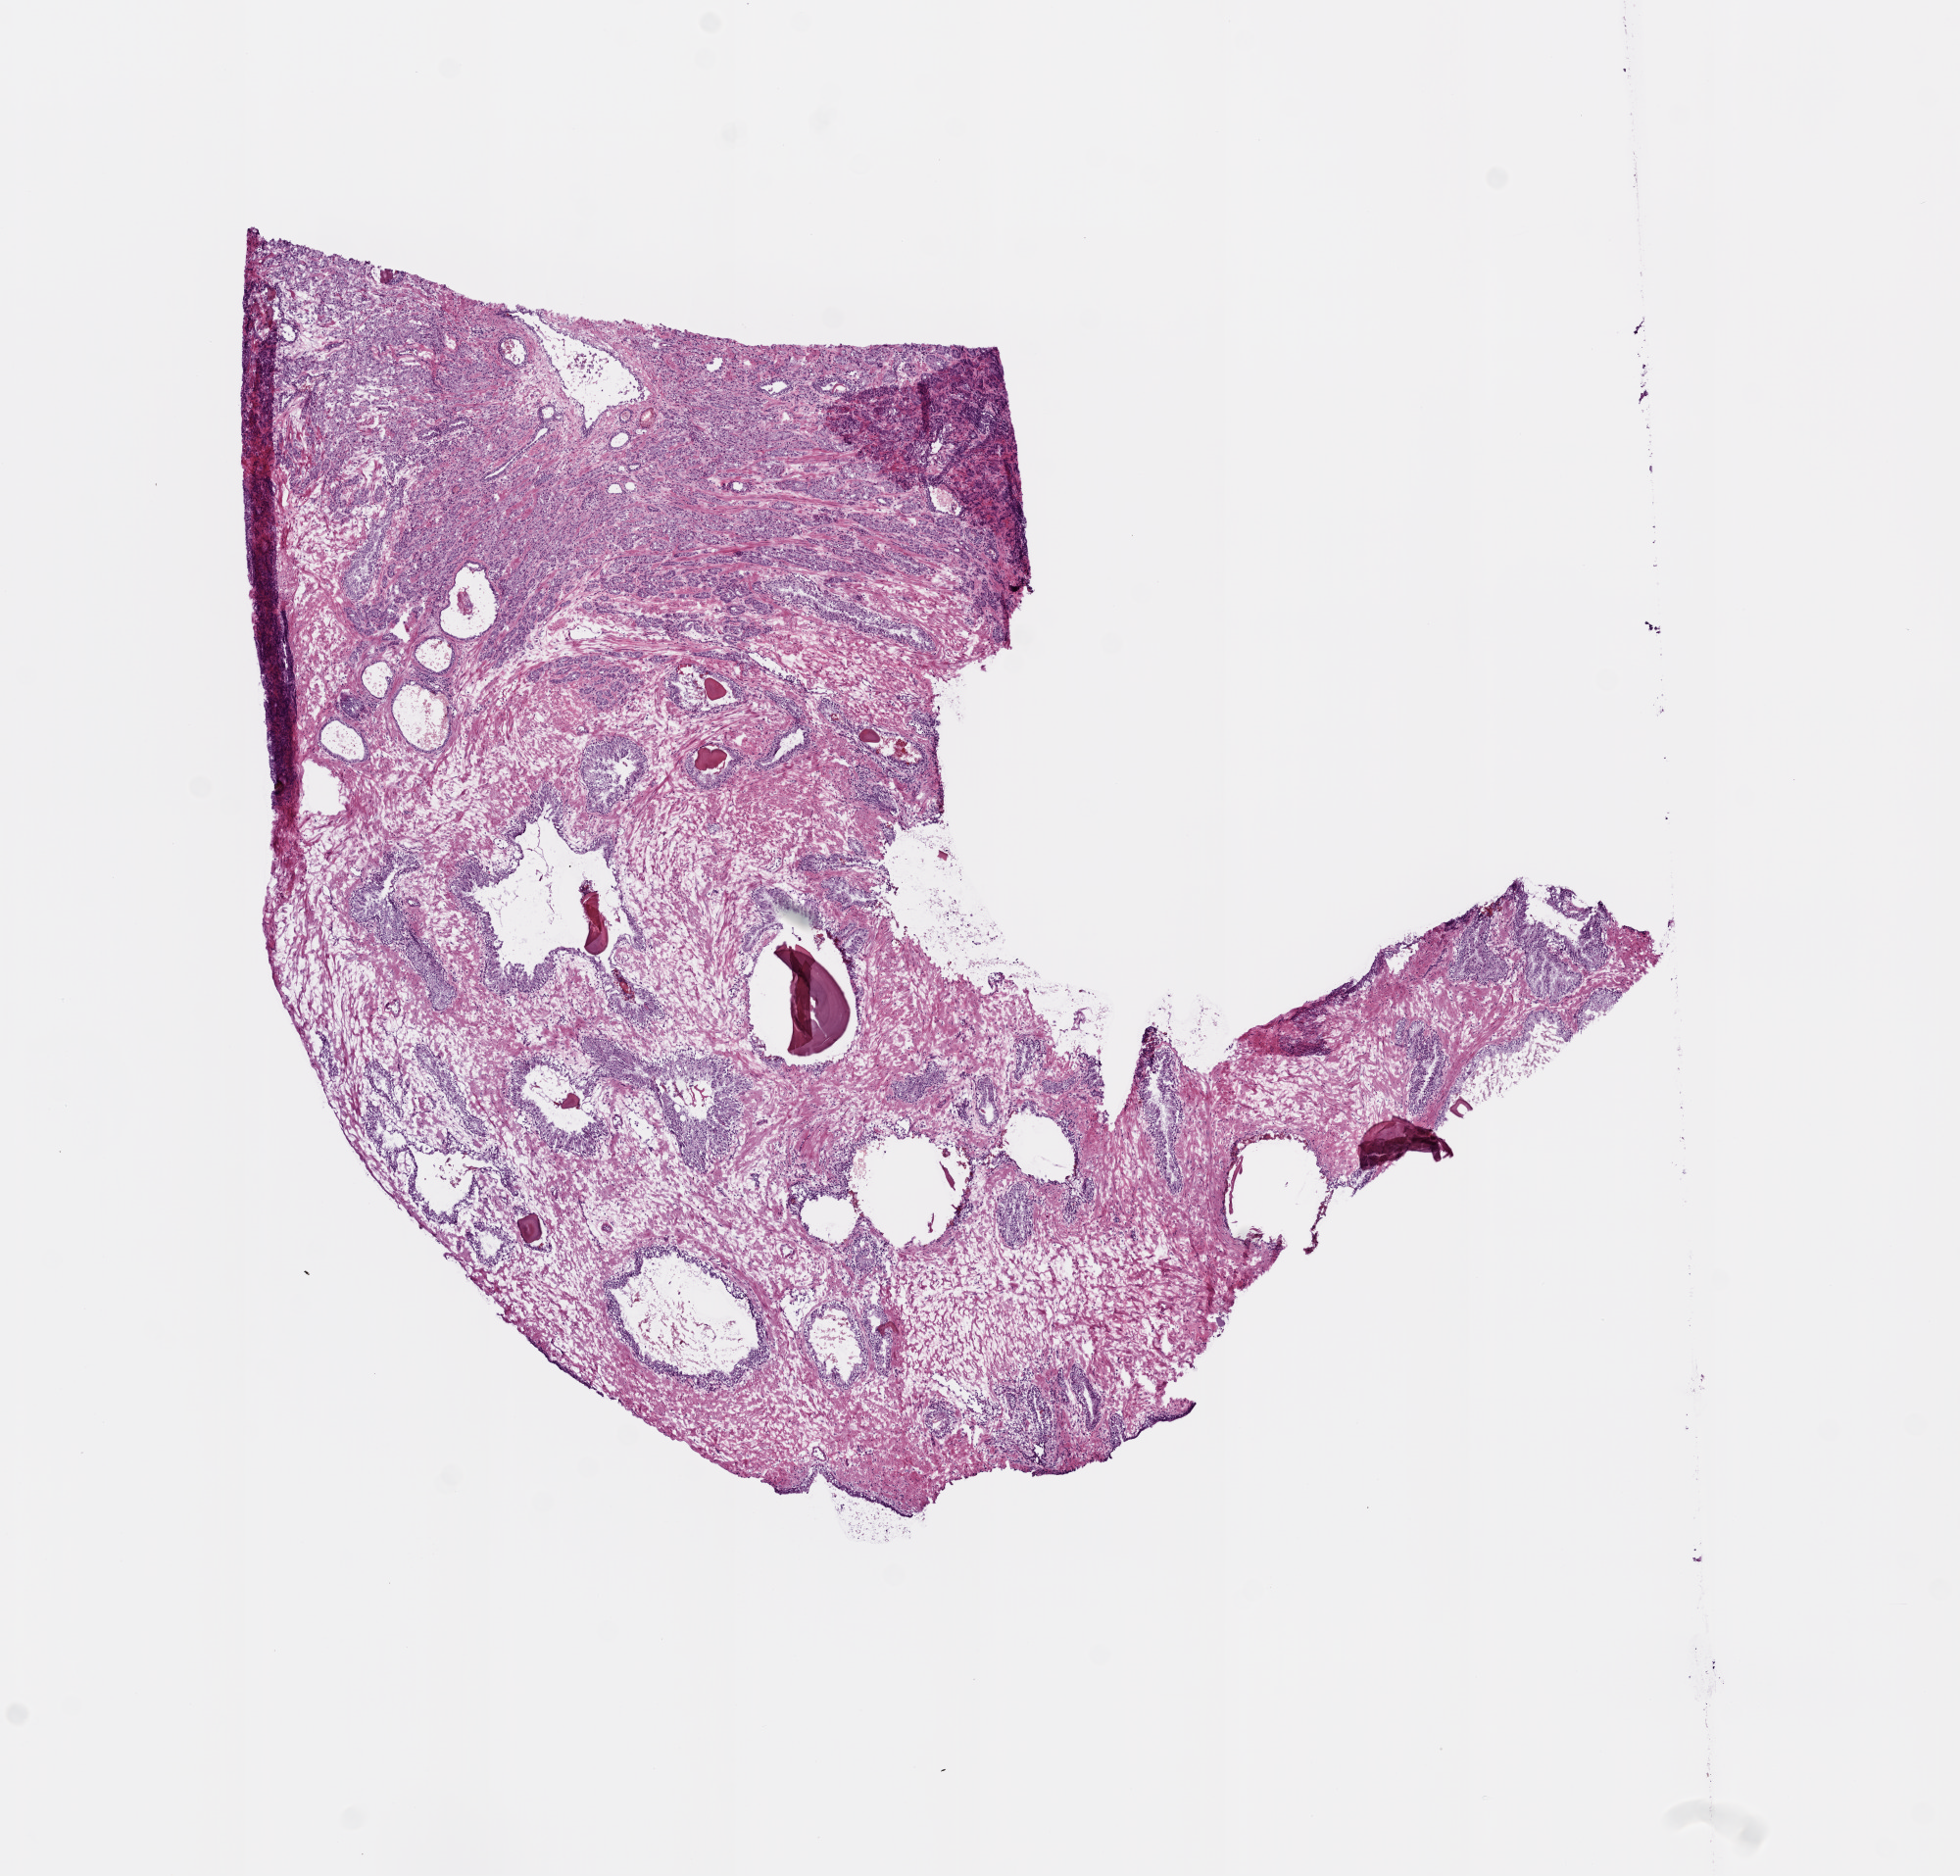
Digitized H&E-stained tissue section (whole slide), low-resolution overview of the scanned area, about 8.0 x 7.7 mm, frozen section, prostate, primary tumour sample. Male patient; age at initial diagnosis 70 years. Gleason score: 9 (4+5). Composition of this section per pathologist review: tumour cells 25%, tumour nuclei 30%, normal cells 20%, stromal cells 55%, necrosis 0%. Inflammatory infiltration, as recorded: lymphocyte infiltration 0%, monocyte infiltration 0%, neutrophil infiltration 0%.
Diagnosis: Acinar cell carcinoma (prostate gland).